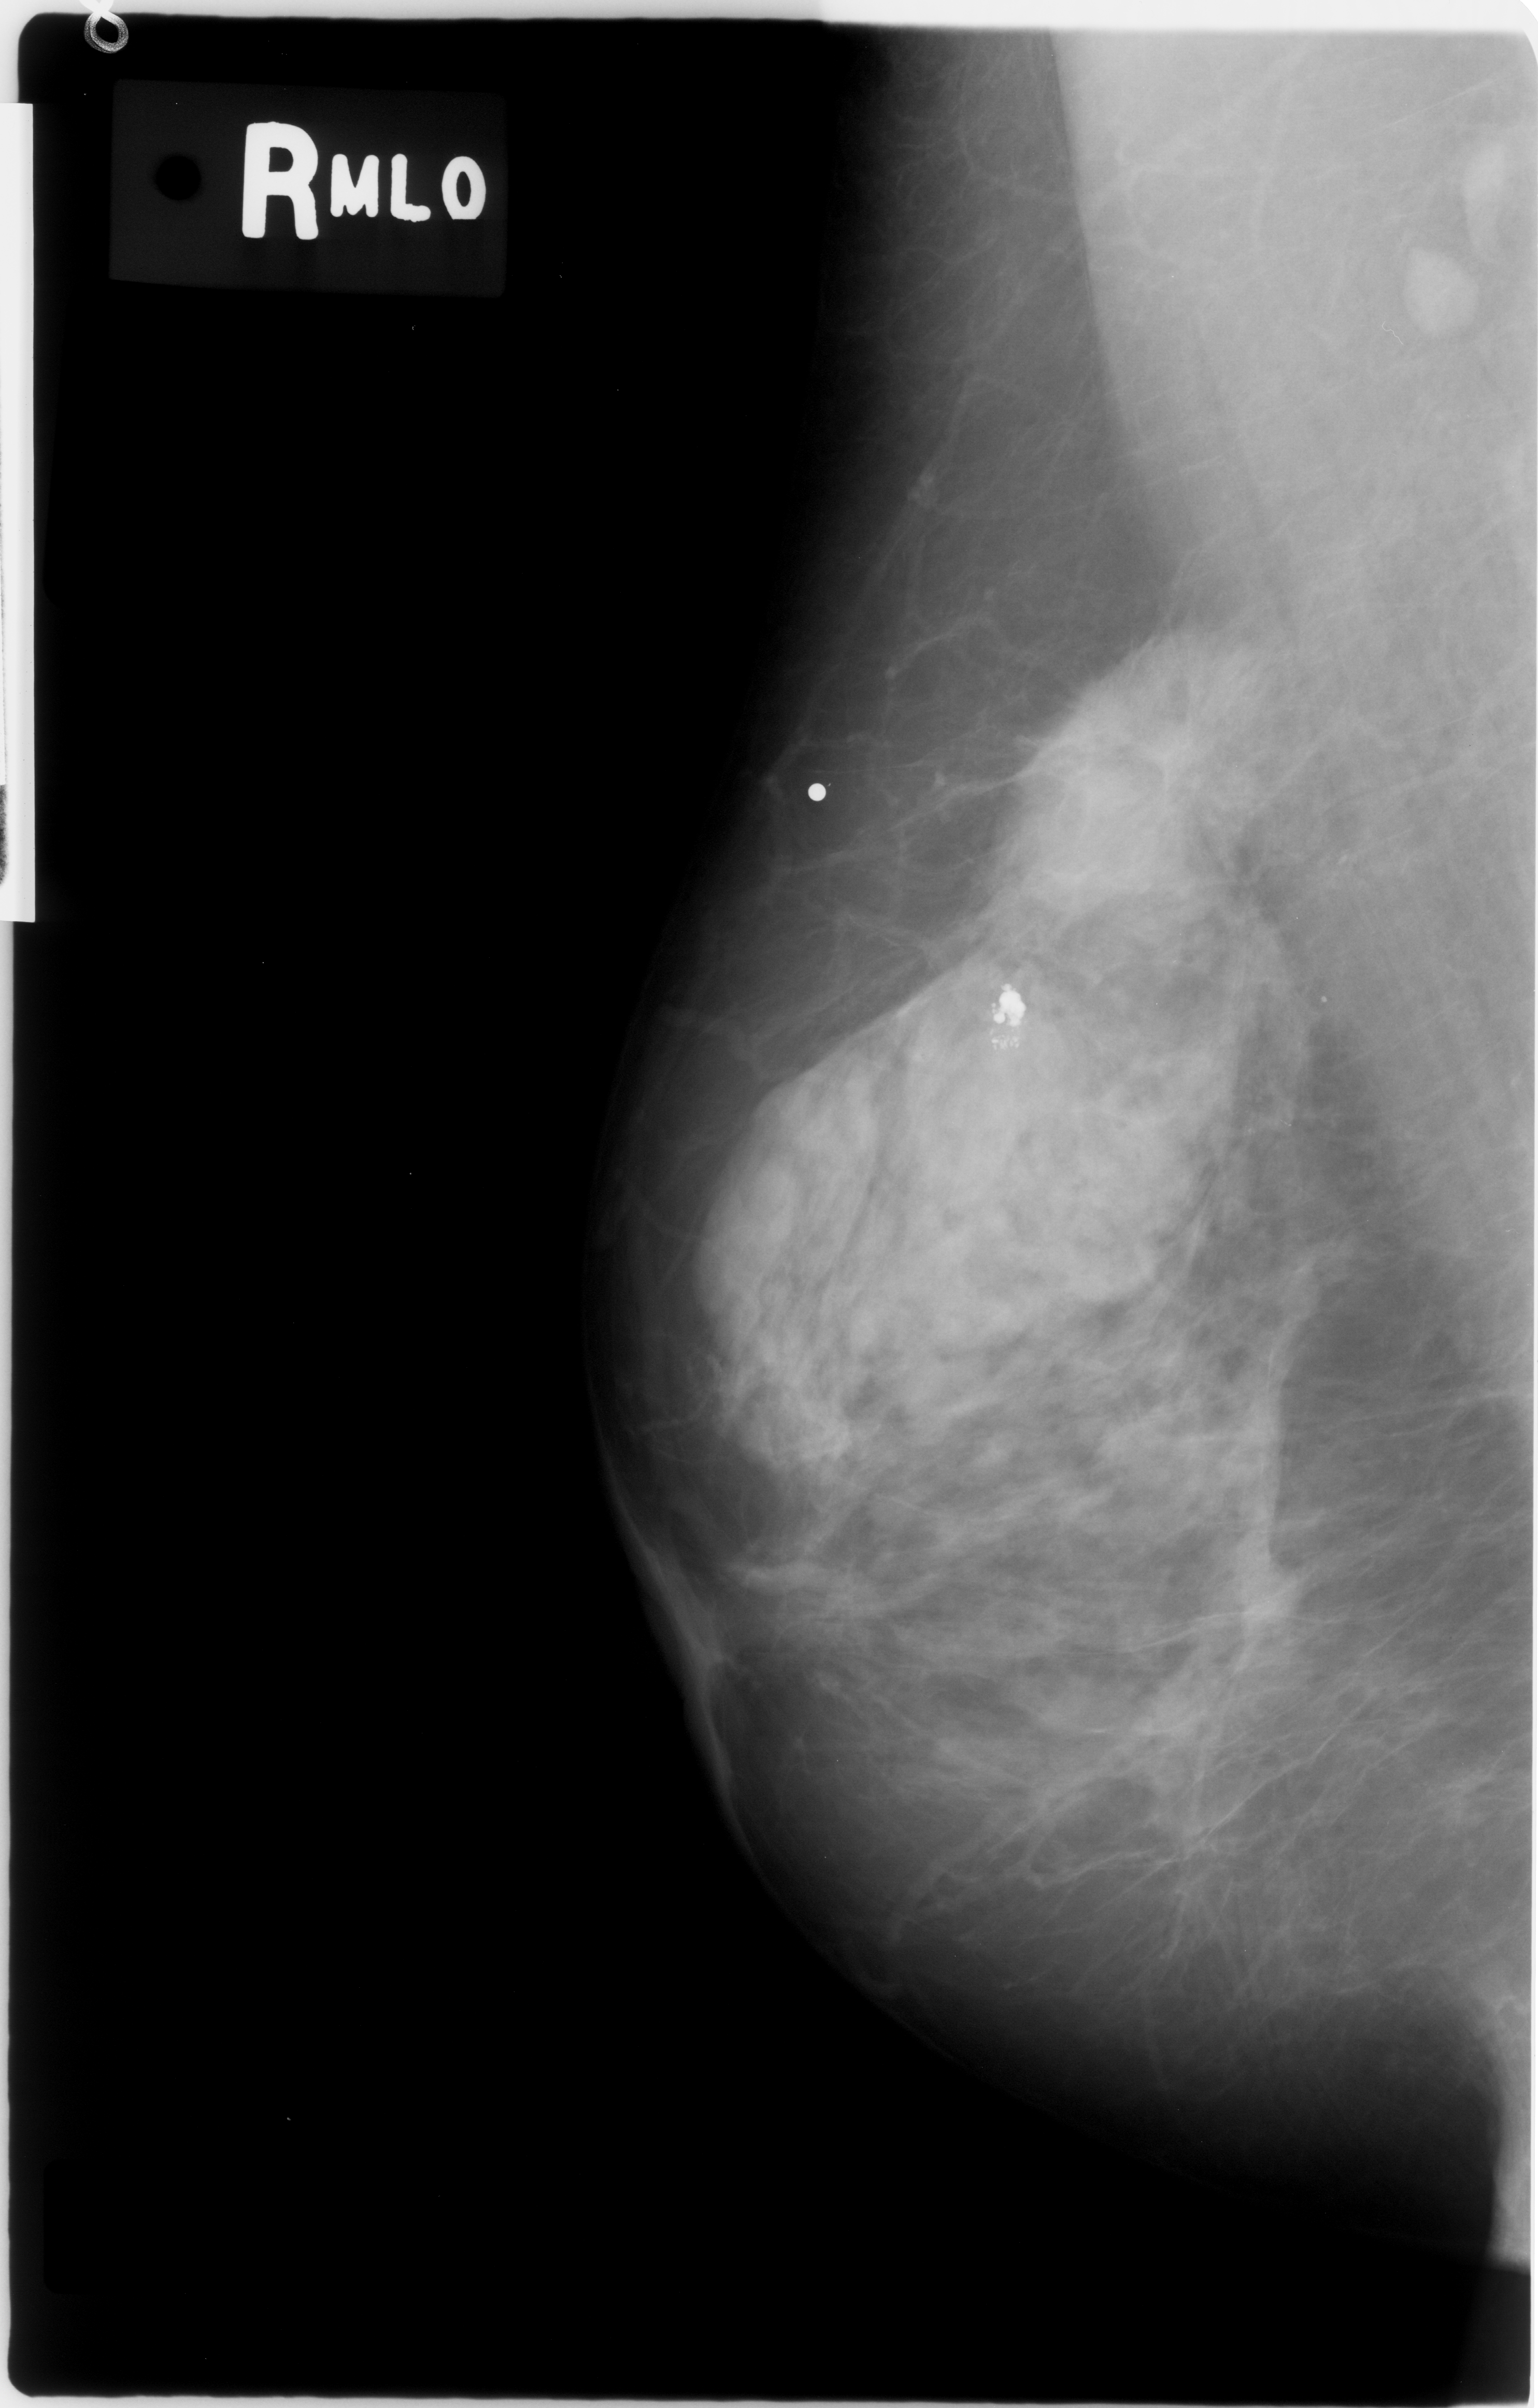
Mammogram (digitized film), right breast, MLO view, breast composition: heterogeneously dense (BI-RADS density category 3 of 4).
Radiologist-marked abnormalities on this image: mass, shape irregular, margins spiculated; BI-RADS assessment category 5; subtlety rating 5 on a 1 (subtle) to 5 (obvious) scale; pathology (as recorded): malignant.